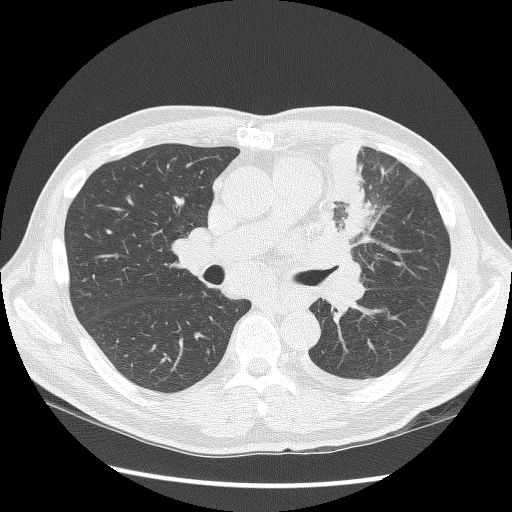
Chest CT (low-dose screening protocol), one axial image. Second annual screen. Lung window (W 1500 / L -600 HU). Slice 55 of 136 in the series. 512 × 512 image matrix. Male participant, aged 64 years at enrolment. Former smoker at enrolment.
- Lesion marked by an expert reader, box from (x=304, y=138) to (x=389, y=281) px.
- No non-calcified nodule or mass ≥4 mm was recorded by the screening reader at this exam.
- Official screen result: positive, other.
- Participant outcome: lung cancer diagnosed 24 days after this screen — small cell carcinoma, NOS, left upper lobe, stage IV (AJCC 6th edition), 100 mm at pathology.